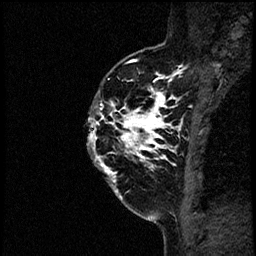
Breast MRI (dynamic contrast-enhanced), one sagittal slice; position 44 of 60 along the scan axis; dynamic contrast-enhanced study with each time point stored as its own series, time point 2 of 4 at this slice position (early post-contrast, ordered by acquisition time); 1.5 T; TE 4.2 ms, TR 17.6 ms; 256 × 256 image matrix. Female patient, age 40 years. Case-level facts recorded for this patient, not image findings: setting: breast cancer imaged before/during neoadjuvant chemotherapy; receptor status: HER2-positive.
Annotated regions visible in this slice (semi-automatic segmentation, software-assisted and operator-edited):
- analysis volume of interest (the breast-tissue region the enhancement analysis was run in; not a lesion): bounding box <88,56,197,205> (left, top, right, bottom; pixels)
- tumour enhancement mask (voxels above the 100 % enhancement threshold inside the analysis volume of interest): <89,60,188,183>